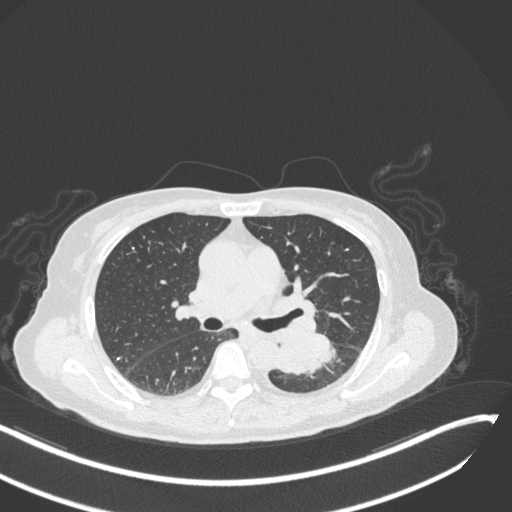
Chest CT, one axial slice; position 165 of 342 along the scan axis; reconstruction kernel B31f; 120 kVp; lung window (W 1500 / L -600 HU); 1 mm slice thickness; 512 × 512 image matrix, field of view 400 × 400 mm. Patient: female, 64 years. Case-level facts recorded for this patient, not image findings: clinical TNM (as recorded): T3 N1 M1.
Outlined on this slice (rectangle marked by the reading radiologist):
- lung tumour (recorded histology: small cell carcinoma): bounding box (x1, y1, x2, y2) in pixels: (278, 335, 338, 378)